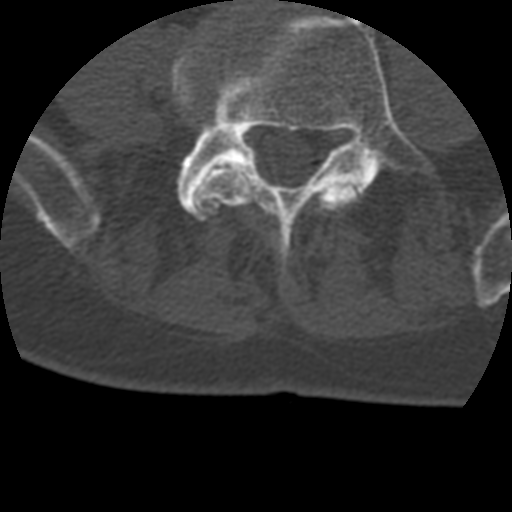
CT including the spine, one axial slice; reconstruction kernel STANDARD; 120 kVp; bone window (W 1800 / L 400 HU); 1.25 mm slice thickness; 512 × 512 image matrix, field of view 160 × 160 mm. Patient age 69 years. Case-level facts recorded for this patient, not image findings: primary cancer: prostate.
Annotated regions visible in this slice (semi-automatic segmentation, software-assisted and operator-edited):
- L4 vertebra: bounding box <171,24,360,253> (left, top, right, bottom; pixels)
- L5 vertebra: <177,11,432,243>